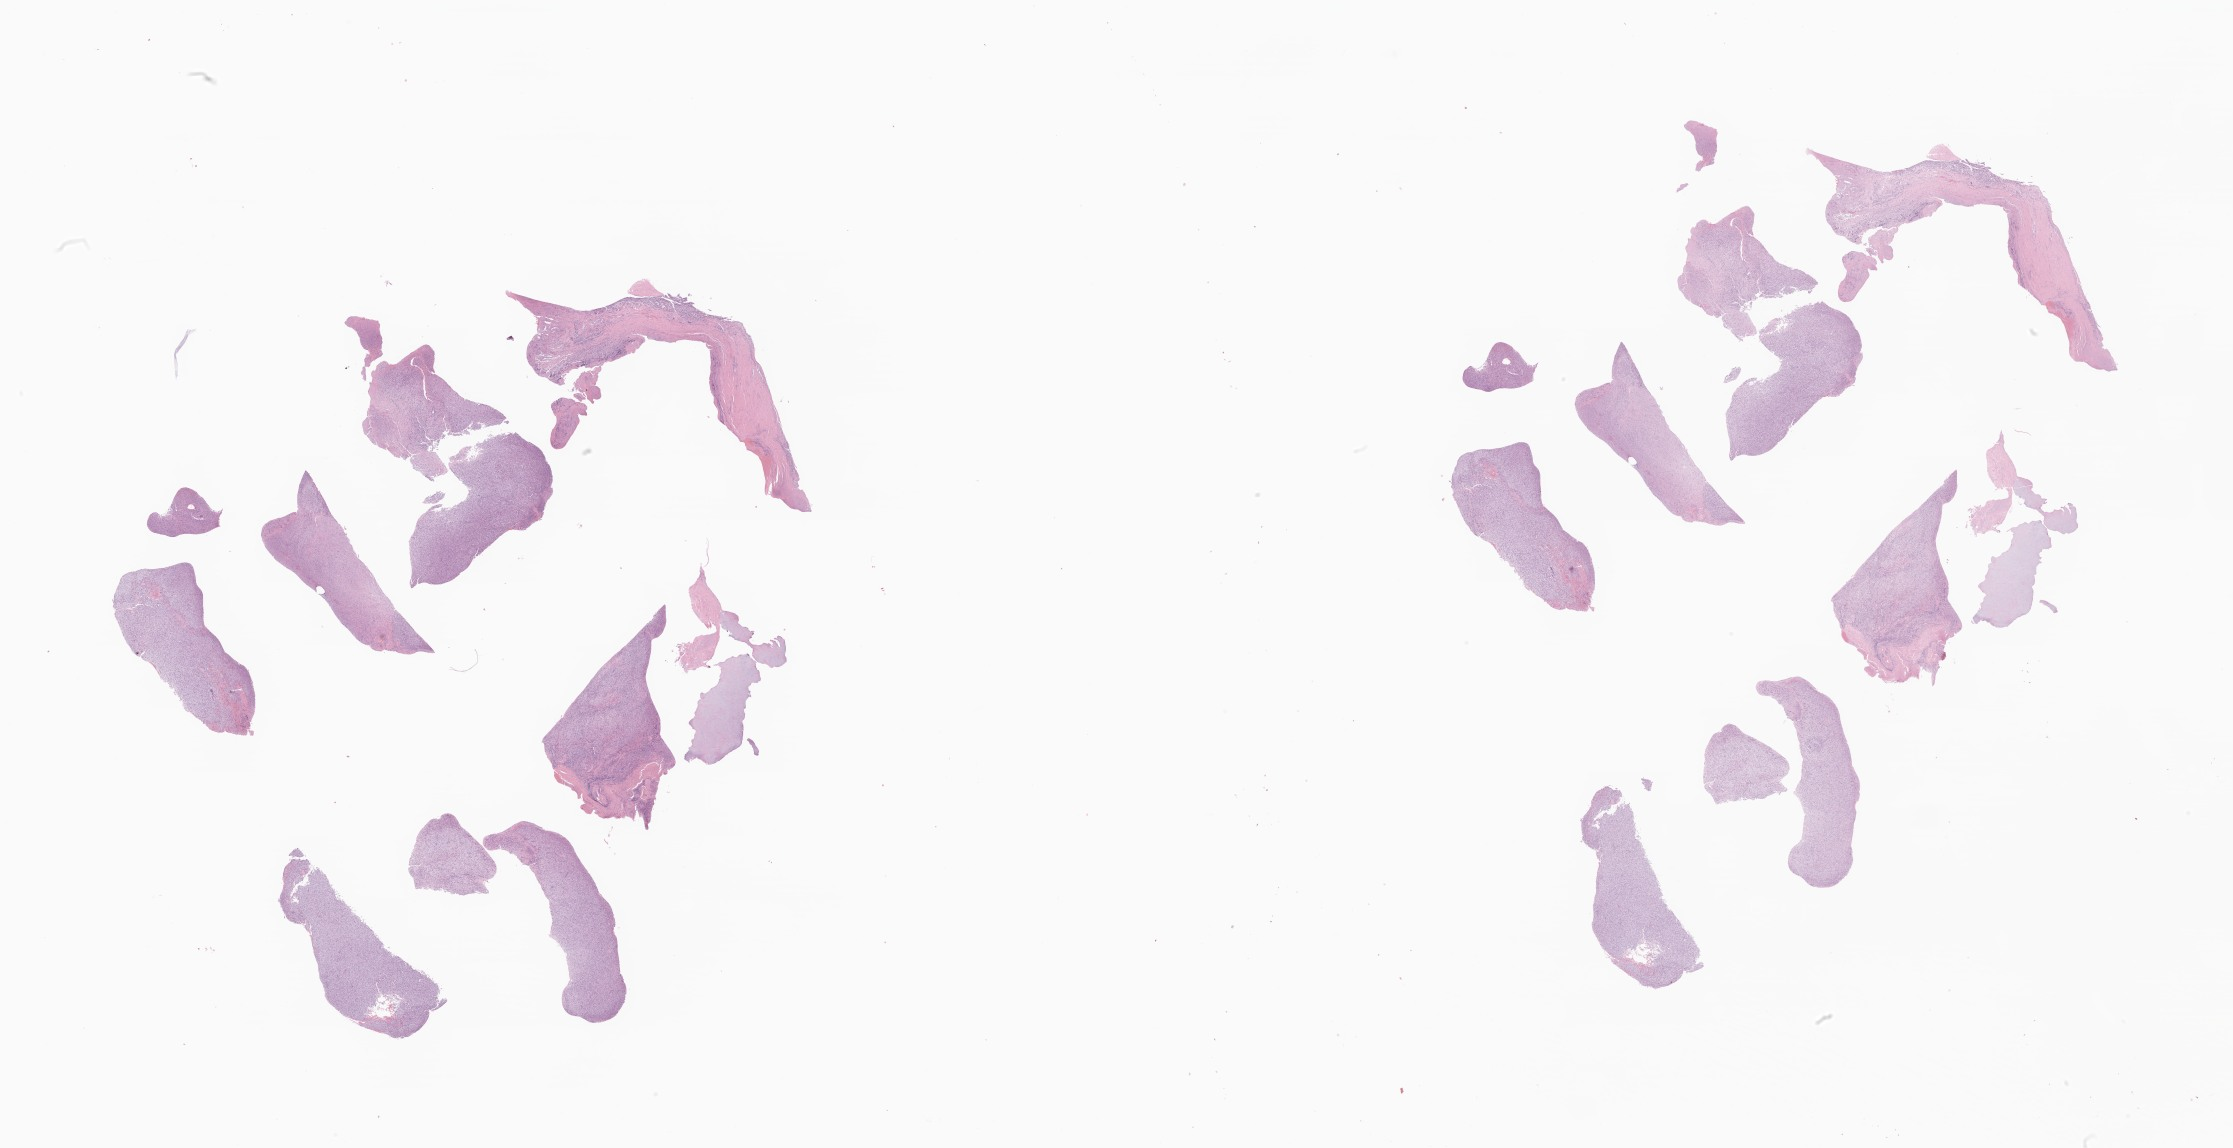
Digitized hematoxylin and eosin (H&E)-stained section of tumor tissue from the central nervous system, shown as a low-resolution overview of the whole scanned area (about 37.7 x 19.4 mm); formalin-fixed, paraffin-embedded (FFPE) tissue. Patient: female, age 276 months.
Diagnosis: Chordoma, NOS.